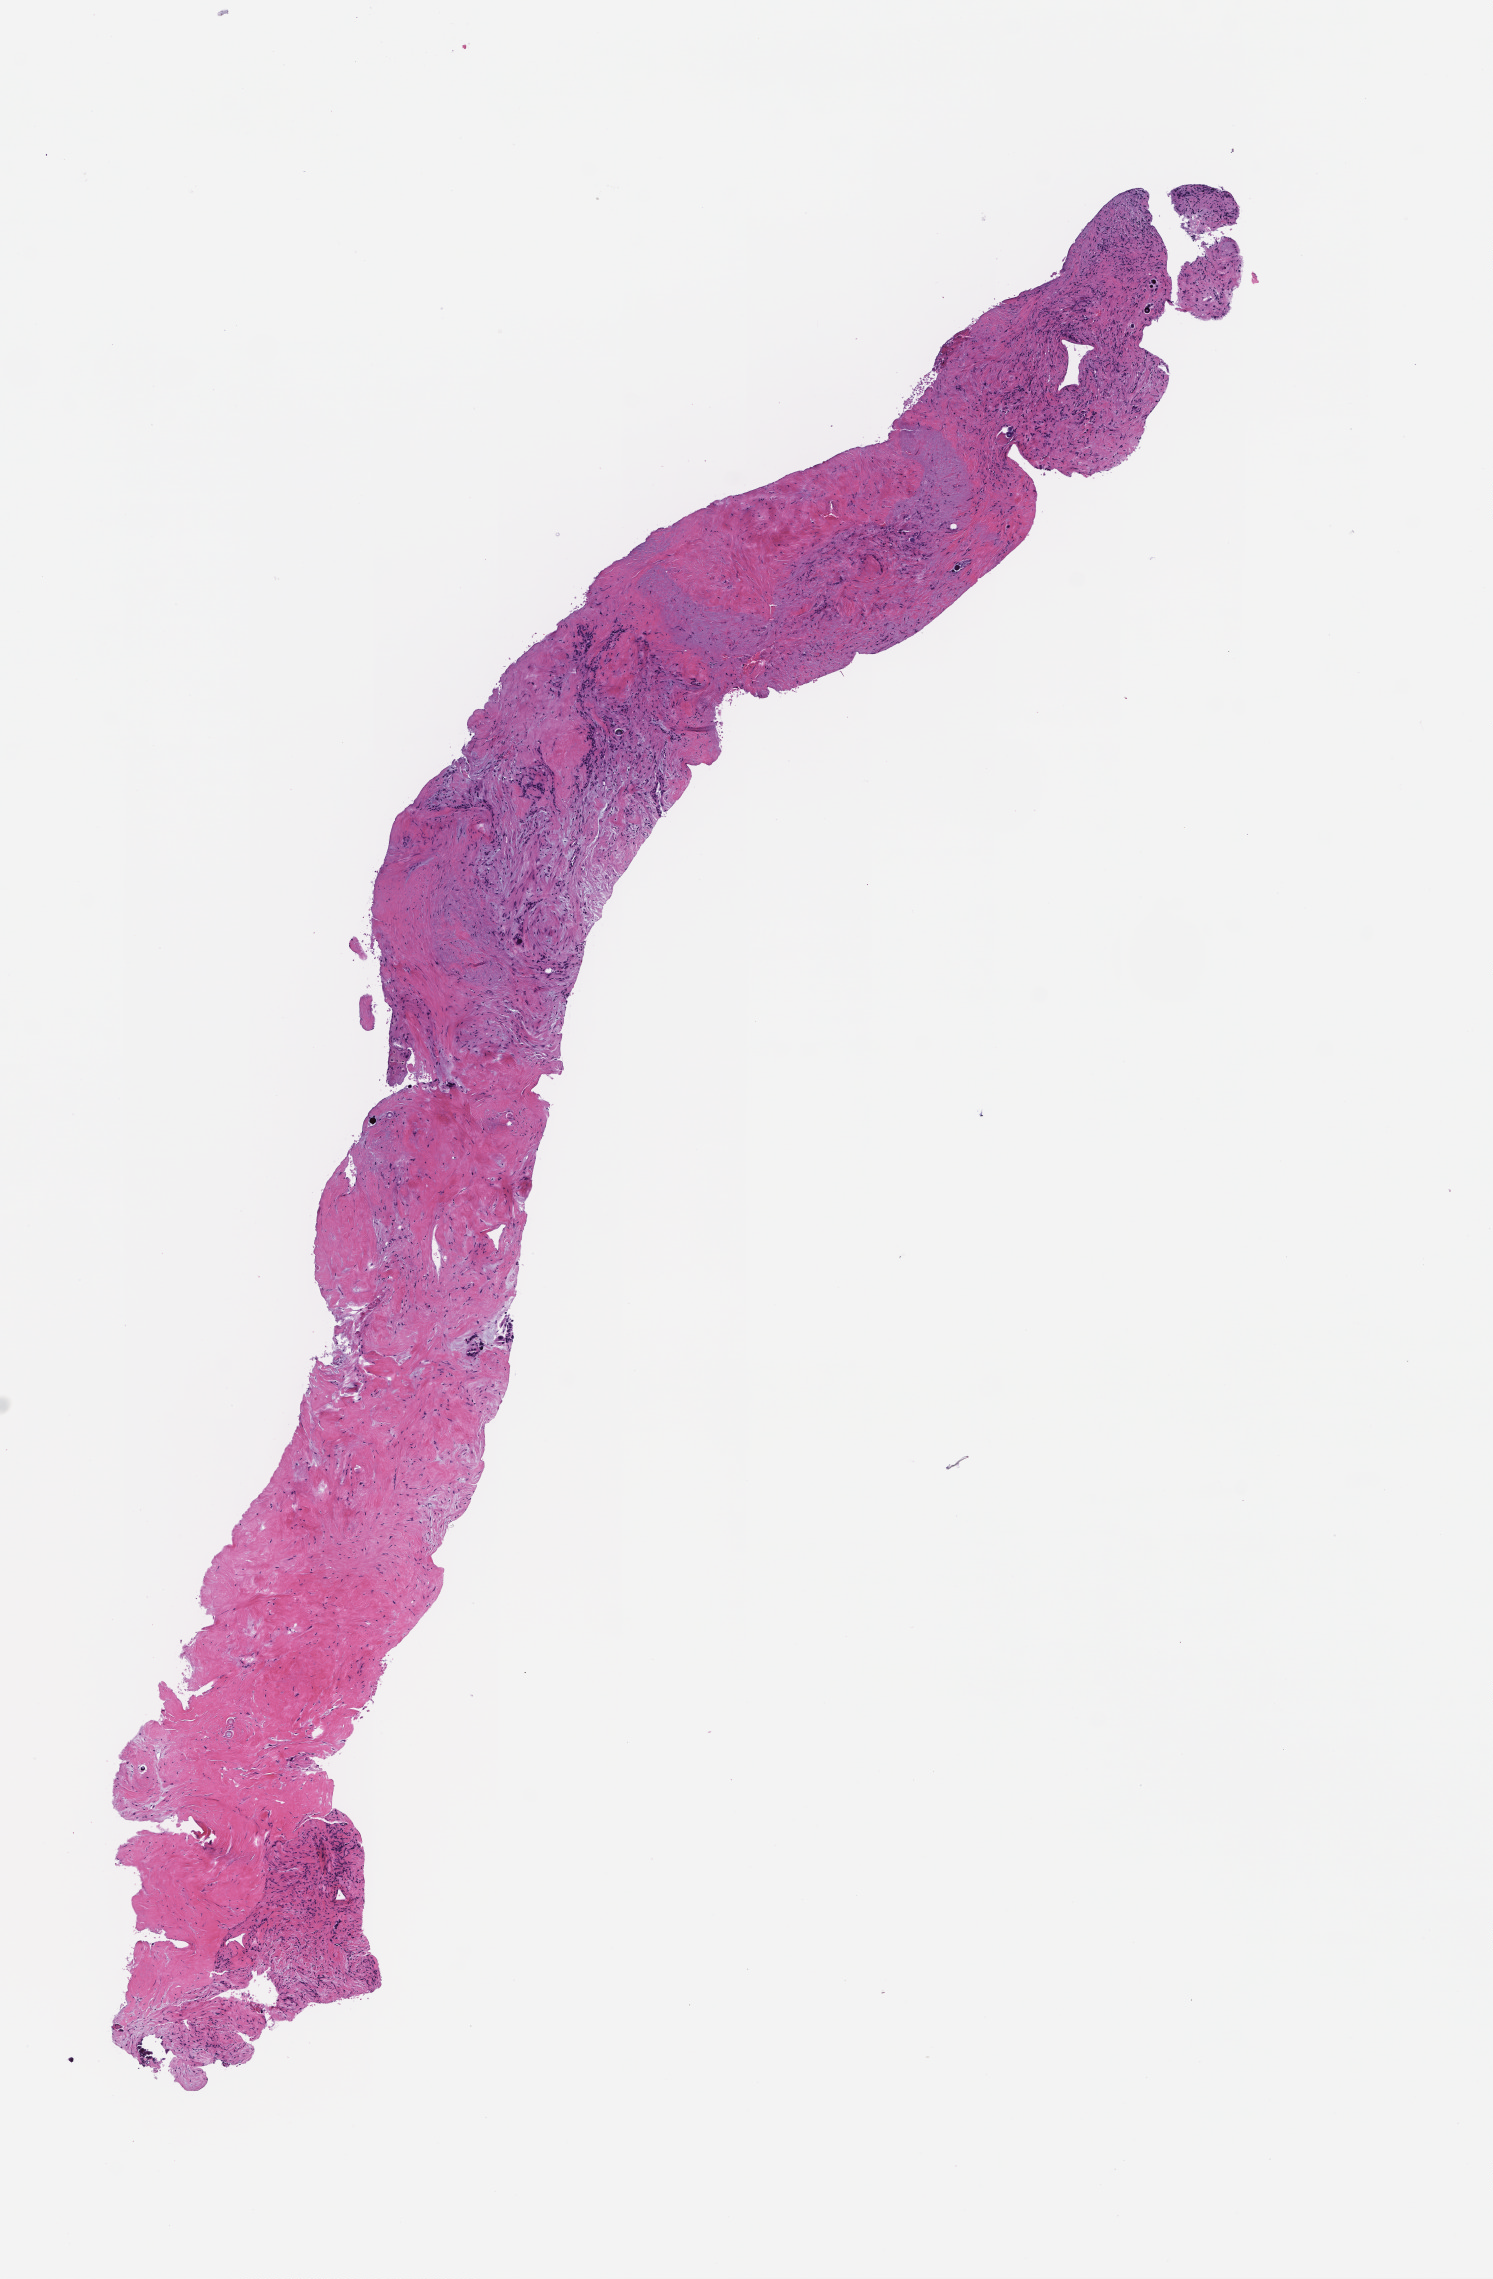
Digitized hematoxylin and eosin (H&E)-stained section — a low-resolution overview of the entire scanned area, about 6.0 x 9.2 mm. FFPE section. Specimen time point: collected at disease progression. Male patient.
This section: metastasis (sampled organ not recorded). Patient diagnosis (primary): Colorectal Carcinoma.